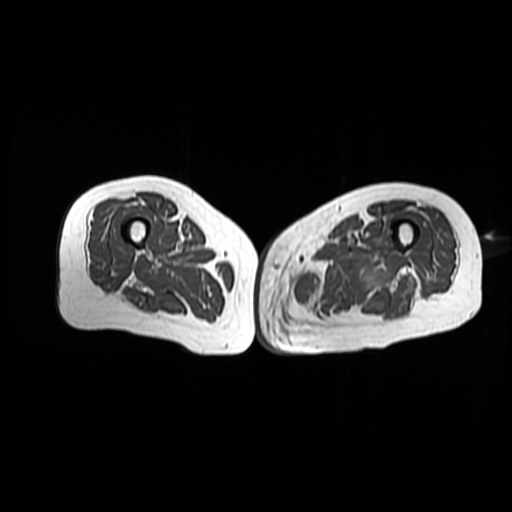
MRI of an extremity soft-tissue mass, one axial slice. Slice 42 of 42 in the series (ordered by position). 512 × 512 image matrix. Female patient. From the clinical record (not read from this slice): histological type: pleomorphic leiomyosarcoma; grade: high; site of the primary tumour: left thigh.
Annotated regions visible in this slice (manually delineated by an expert):
- gross tumour volume including surrounding oedema: bounding box <293,270,325,294> (left, top, right, bottom; pixels)